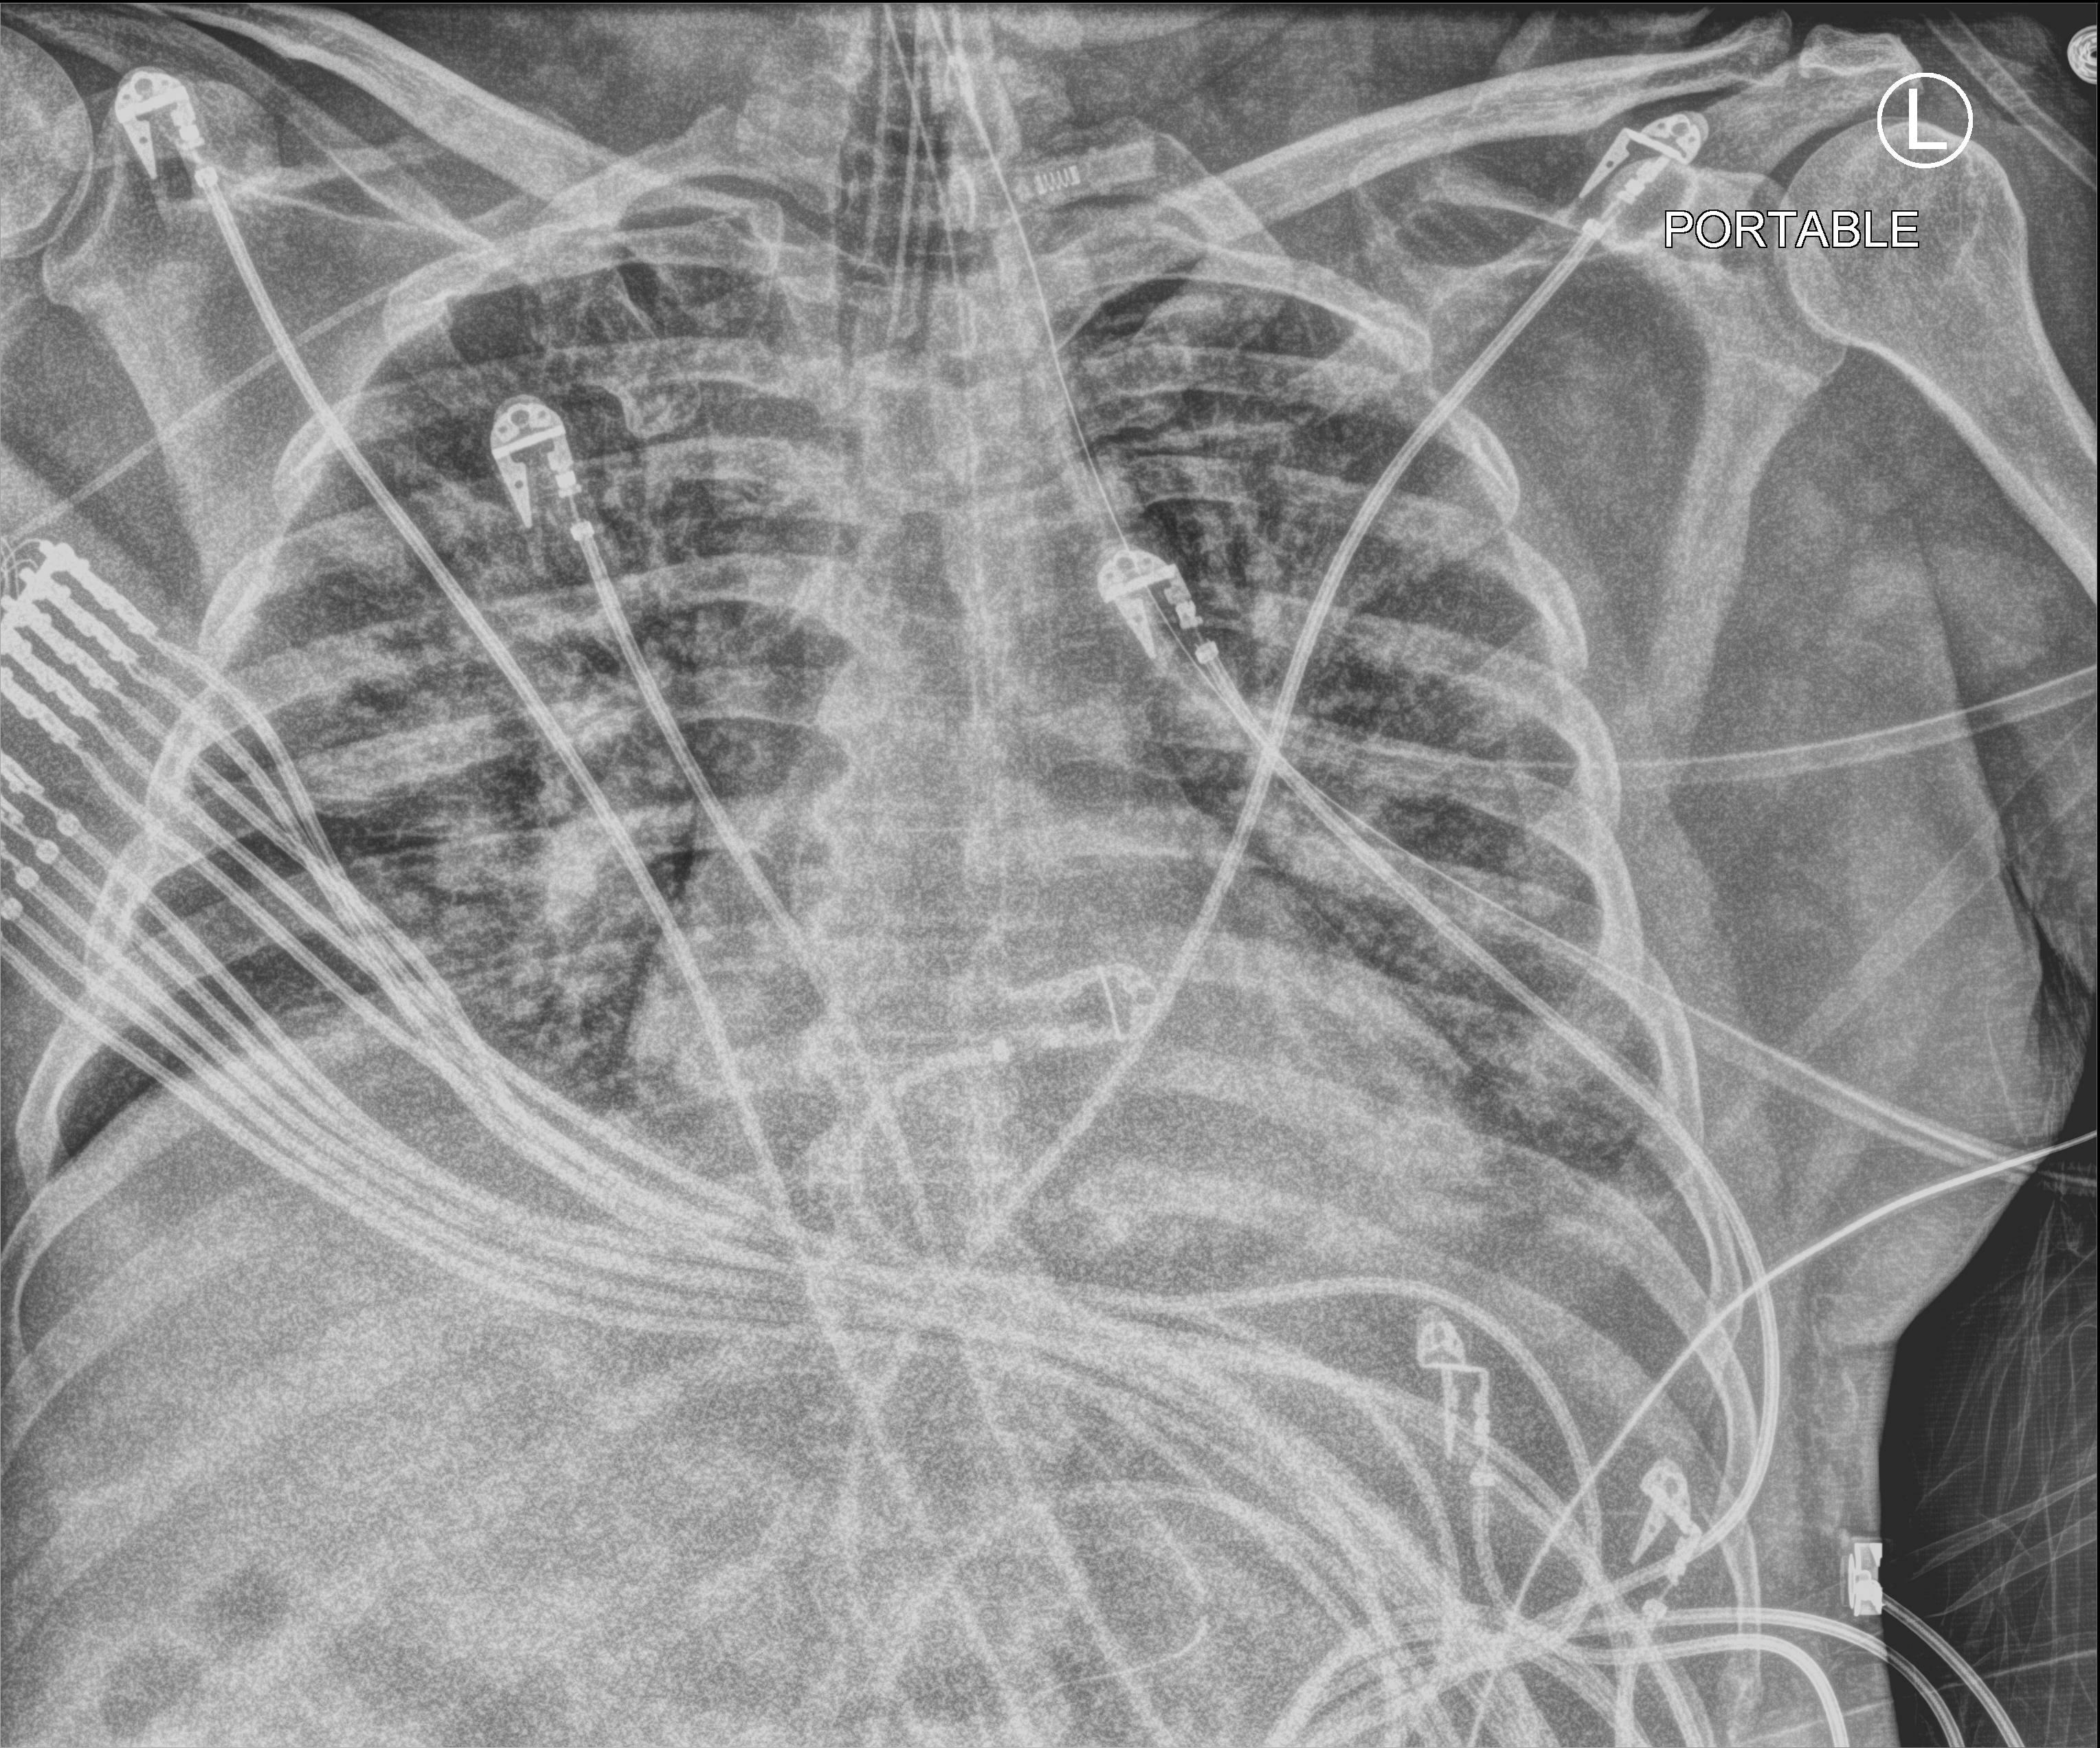
Bedside chest radiograph (computed radiography); anteroposterior (AP) projection. Patient hospitalised with COVID-19; male, aged 18–59 years.
Admission-level facts for this patient (not findings on this image; timing relative to this image not recorded): mechanically ventilated during this hospital stay: yes; length of hospital stay: 26 days.